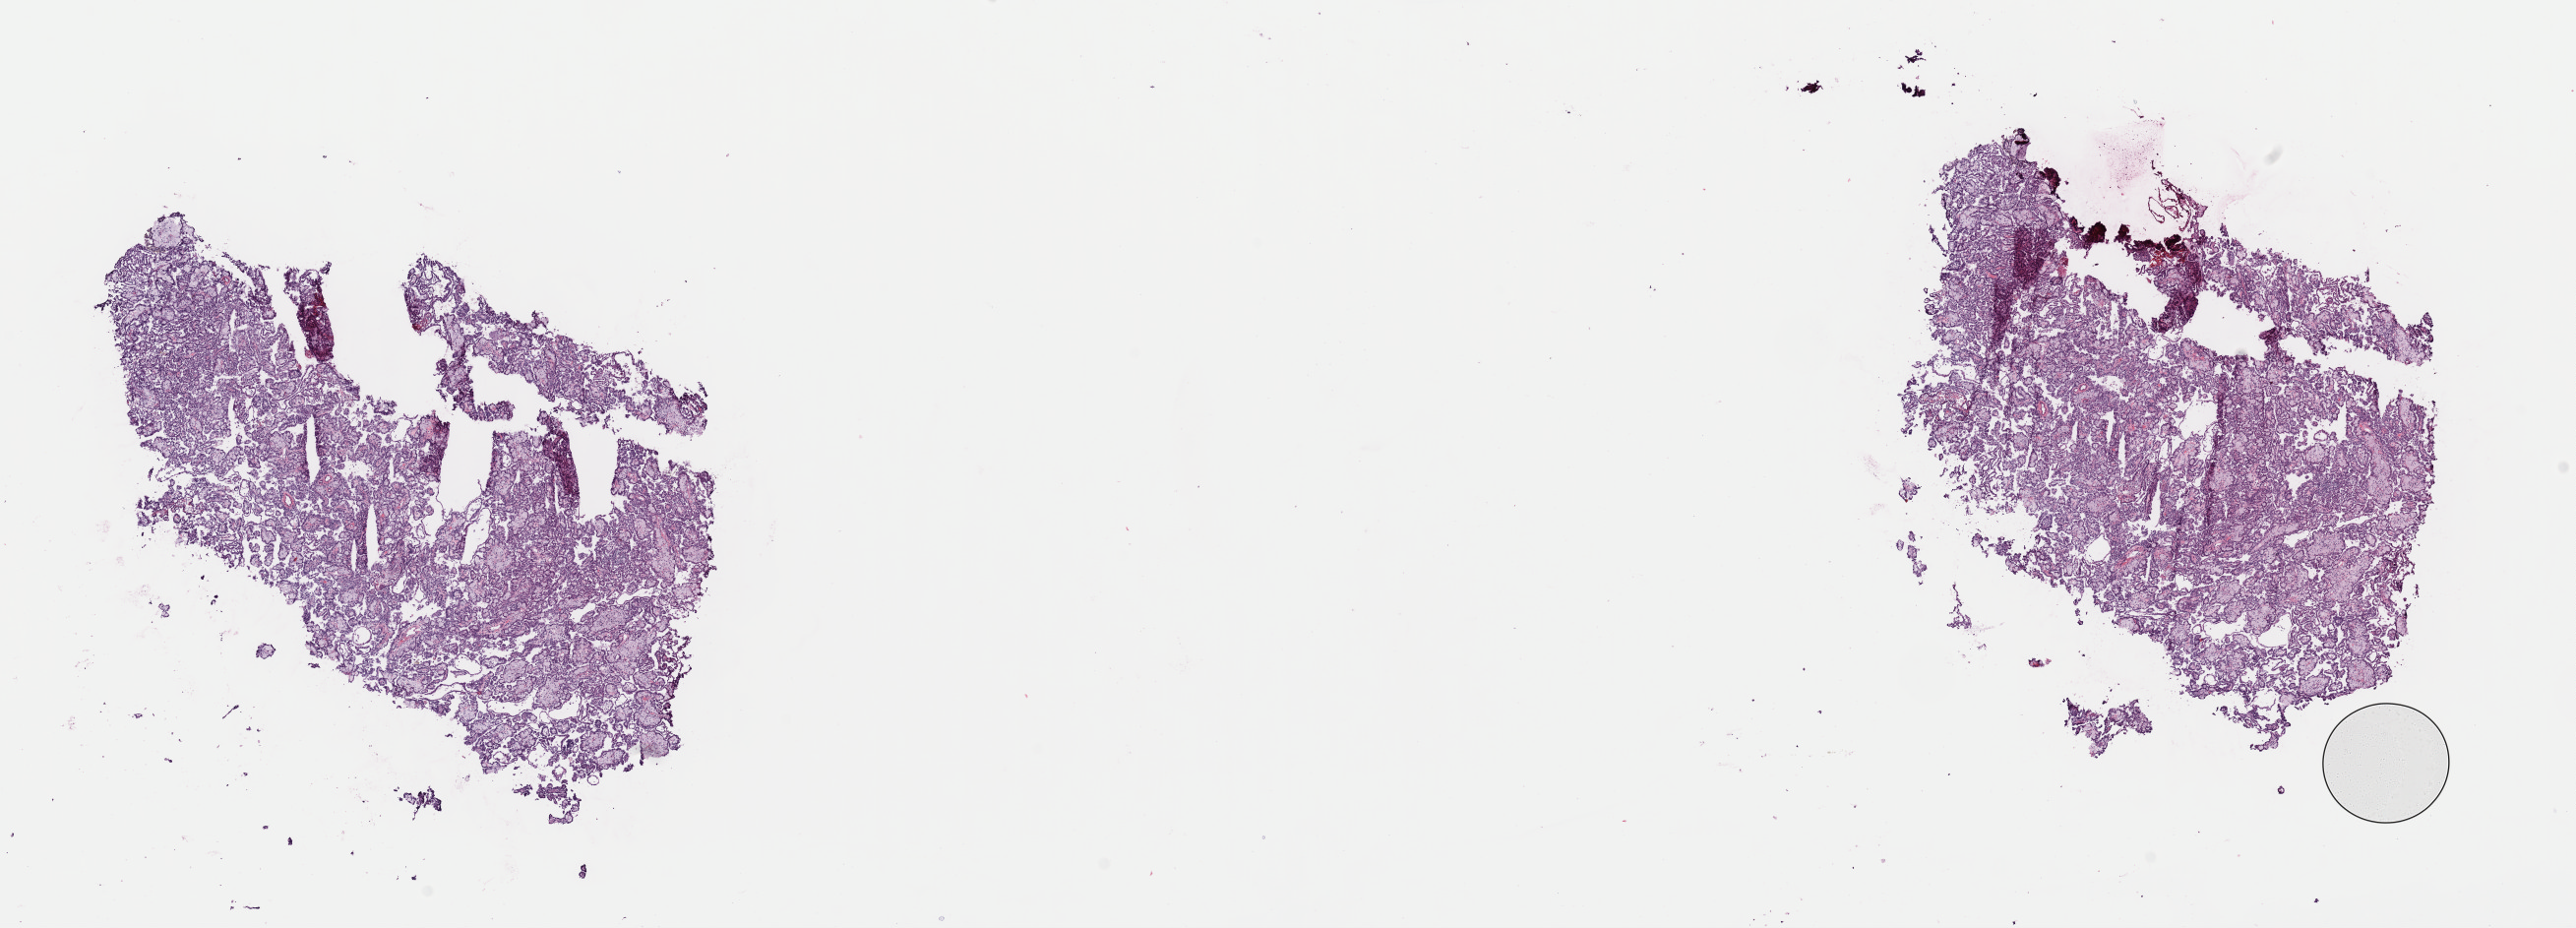
Digitized H&E tissue section (whole slide) — low-resolution overview of the scanned area, about 20.7 x 7.4 mm; frozen section from the top of the tissue portion; kidney, primary tumour sample. Patient: male, age at initial diagnosis 39 years. Pathologist review of this section (percent, as recorded): tumour cells 70%, tumour nuclei 80%, normal cells 0%, stromal cells 30%, necrosis 0%. Inflammatory infiltration, as recorded: lymphocyte infiltration 0%, monocyte infiltration 0%, neutrophil infiltration 0%.
* diagnosis: Papillary adenocarcinoma, NOS
* AJCC pathologic stage: I (7th edition)